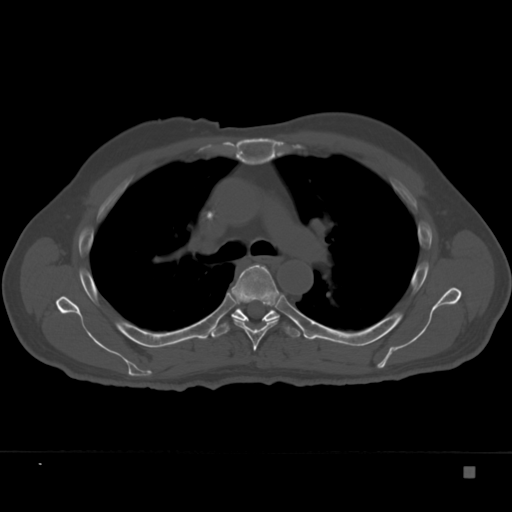
CT including the spine, one axial slice; position 250 of 332 along the scan axis; bone window (W 1800 / L 400 HU); 1.5 mm slice thickness; 512 × 512 image matrix, field of view 389 × 389 mm. Patient: male, 72 years. Case-level facts recorded for this patient, not image findings: primary cancer: skeletal.
Structures marked on this image (semi-automatically segmented with operator editing):
- T5 vertebra: box from (x=228, y=264) to (x=283, y=351) px
- T6 vertebra: (x=211, y=308)–(x=300, y=338)